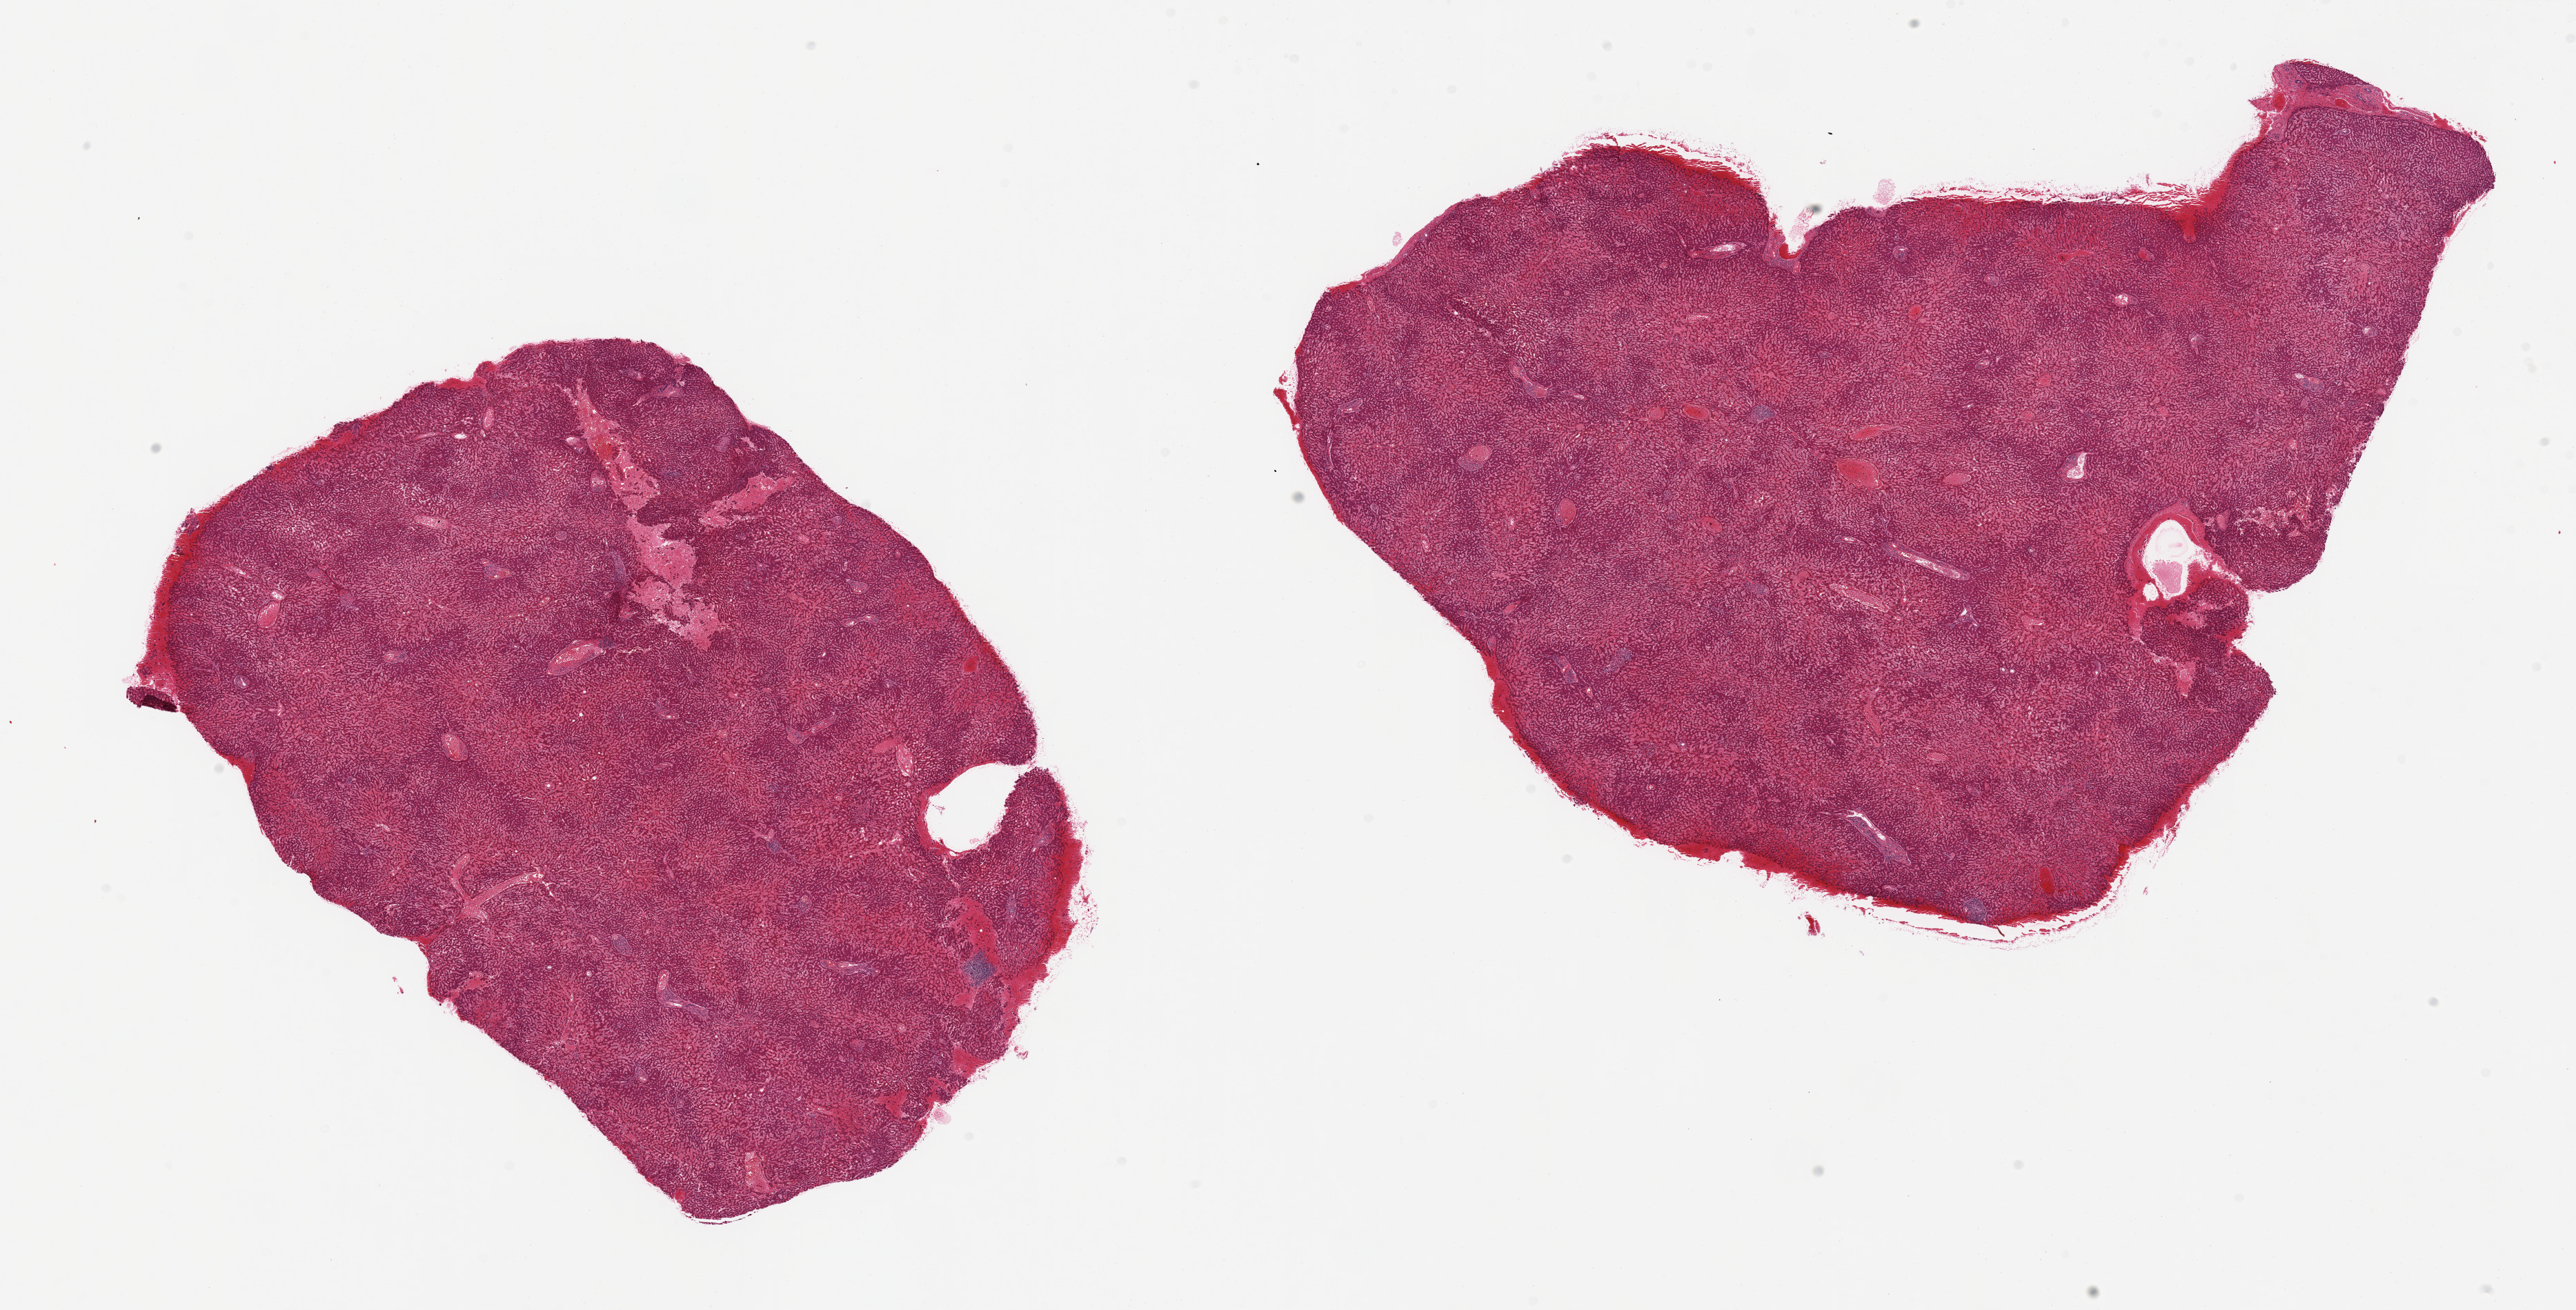
Whole-slide image, hematoxylin and eosin (H&E) stain, a low-resolution overview of the entire scanned area, about 29.5 x 15.0 mm. PAXgene-fixed paraffin-embedded (PFPE) section. Section of liver (target tissue). Tissue donor sample. Donor sex: male.
* reviewer comment on this tissue sample: 2 pieces; moderate central passive congestion; 3.5x1mm focus of hemorrhage and fragmentation, (traumatic resuscitation, injury?)